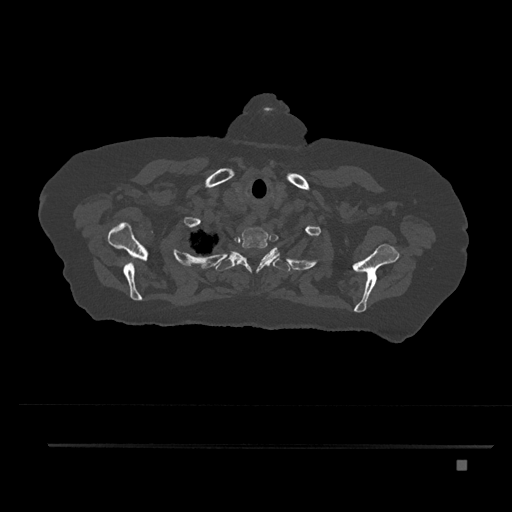
CT including the spine, one axial slice; slice 685 of 797 in the series (ordered by position); 120 kVp; bone window (W 1800 / L 400 HU); 0.5 mm slice thickness; 512 × 512 image matrix, field of view 437 × 437 mm. Patient: female, 76 years. From the clinical record (not read from this slice): primary cancer: lung.
Structures marked on this image (semi-automatic segmentation, software-assisted and operator-edited):
- T1 vertebra: box from (x=235, y=227) to (x=279, y=272) px
- T2 vertebra: (x=207, y=247)–(x=290, y=272)